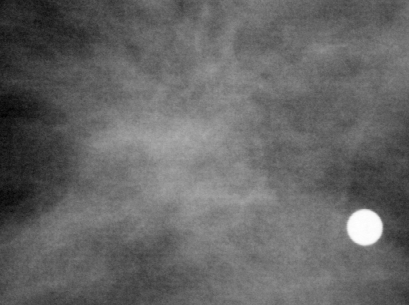
Region of interest cut from a scanned film mammogram (one marked finding), left breast, CC view.
Marked abnormality: mass, shape architectural distortion, margins spiculated; BI-RADS assessment category 5; pathology result (as recorded, not read from the image): malignant.